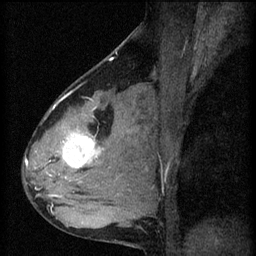
Breast MRI (dynamic contrast-enhanced), one sagittal slice; slice 38 of 60 in the series (ordered by position); 3 images stored at this slice position (order not interpretable as contrast timing); 1.5 T; TE 4.2 ms, TR 8.2 ms; 2 mm slice thickness; 256 × 256 image matrix. Patient: female, 37 years.
Structures marked on this image (semi-automatic segmentation, software-assisted and operator-edited):
- analysis volume of interest (the breast-tissue region the enhancement analysis was run in; not a lesion): bounding box [x1, y1, x2, y2] px = [44, 100, 119, 197]
- tumour enhancement mask (voxels above the 70 % enhancement threshold inside the analysis volume of interest): [50, 130, 104, 197]